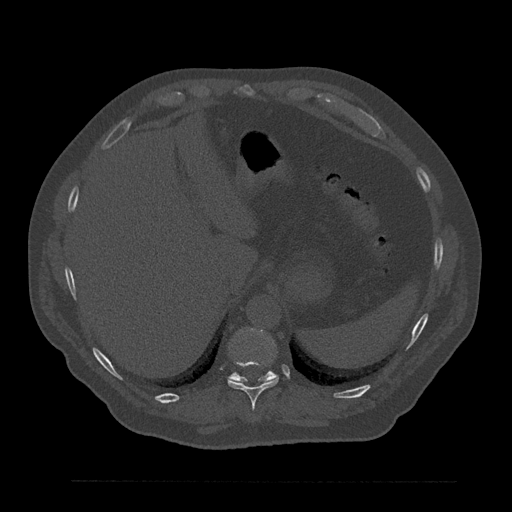
CT including the spine, one axial slice. Slice 330 of 797 in the series (ordered by position). Reconstruction kernel Br40s/3. 120 kVp. Bone window (W 1800 / L 400 HU). 0.5 mm slice thickness. 512 × 512 image matrix, field of view 430 × 430 mm. Patient: male, 61 years. From the clinical record (not read from this slice): primary cancer: prostate.
Outlined on this slice (semi-automatically segmented with operator editing):
- T10 vertebra: box from (x=227, y=360) to (x=279, y=409) px
- T11 vertebra: (x=229, y=331)–(x=276, y=382)